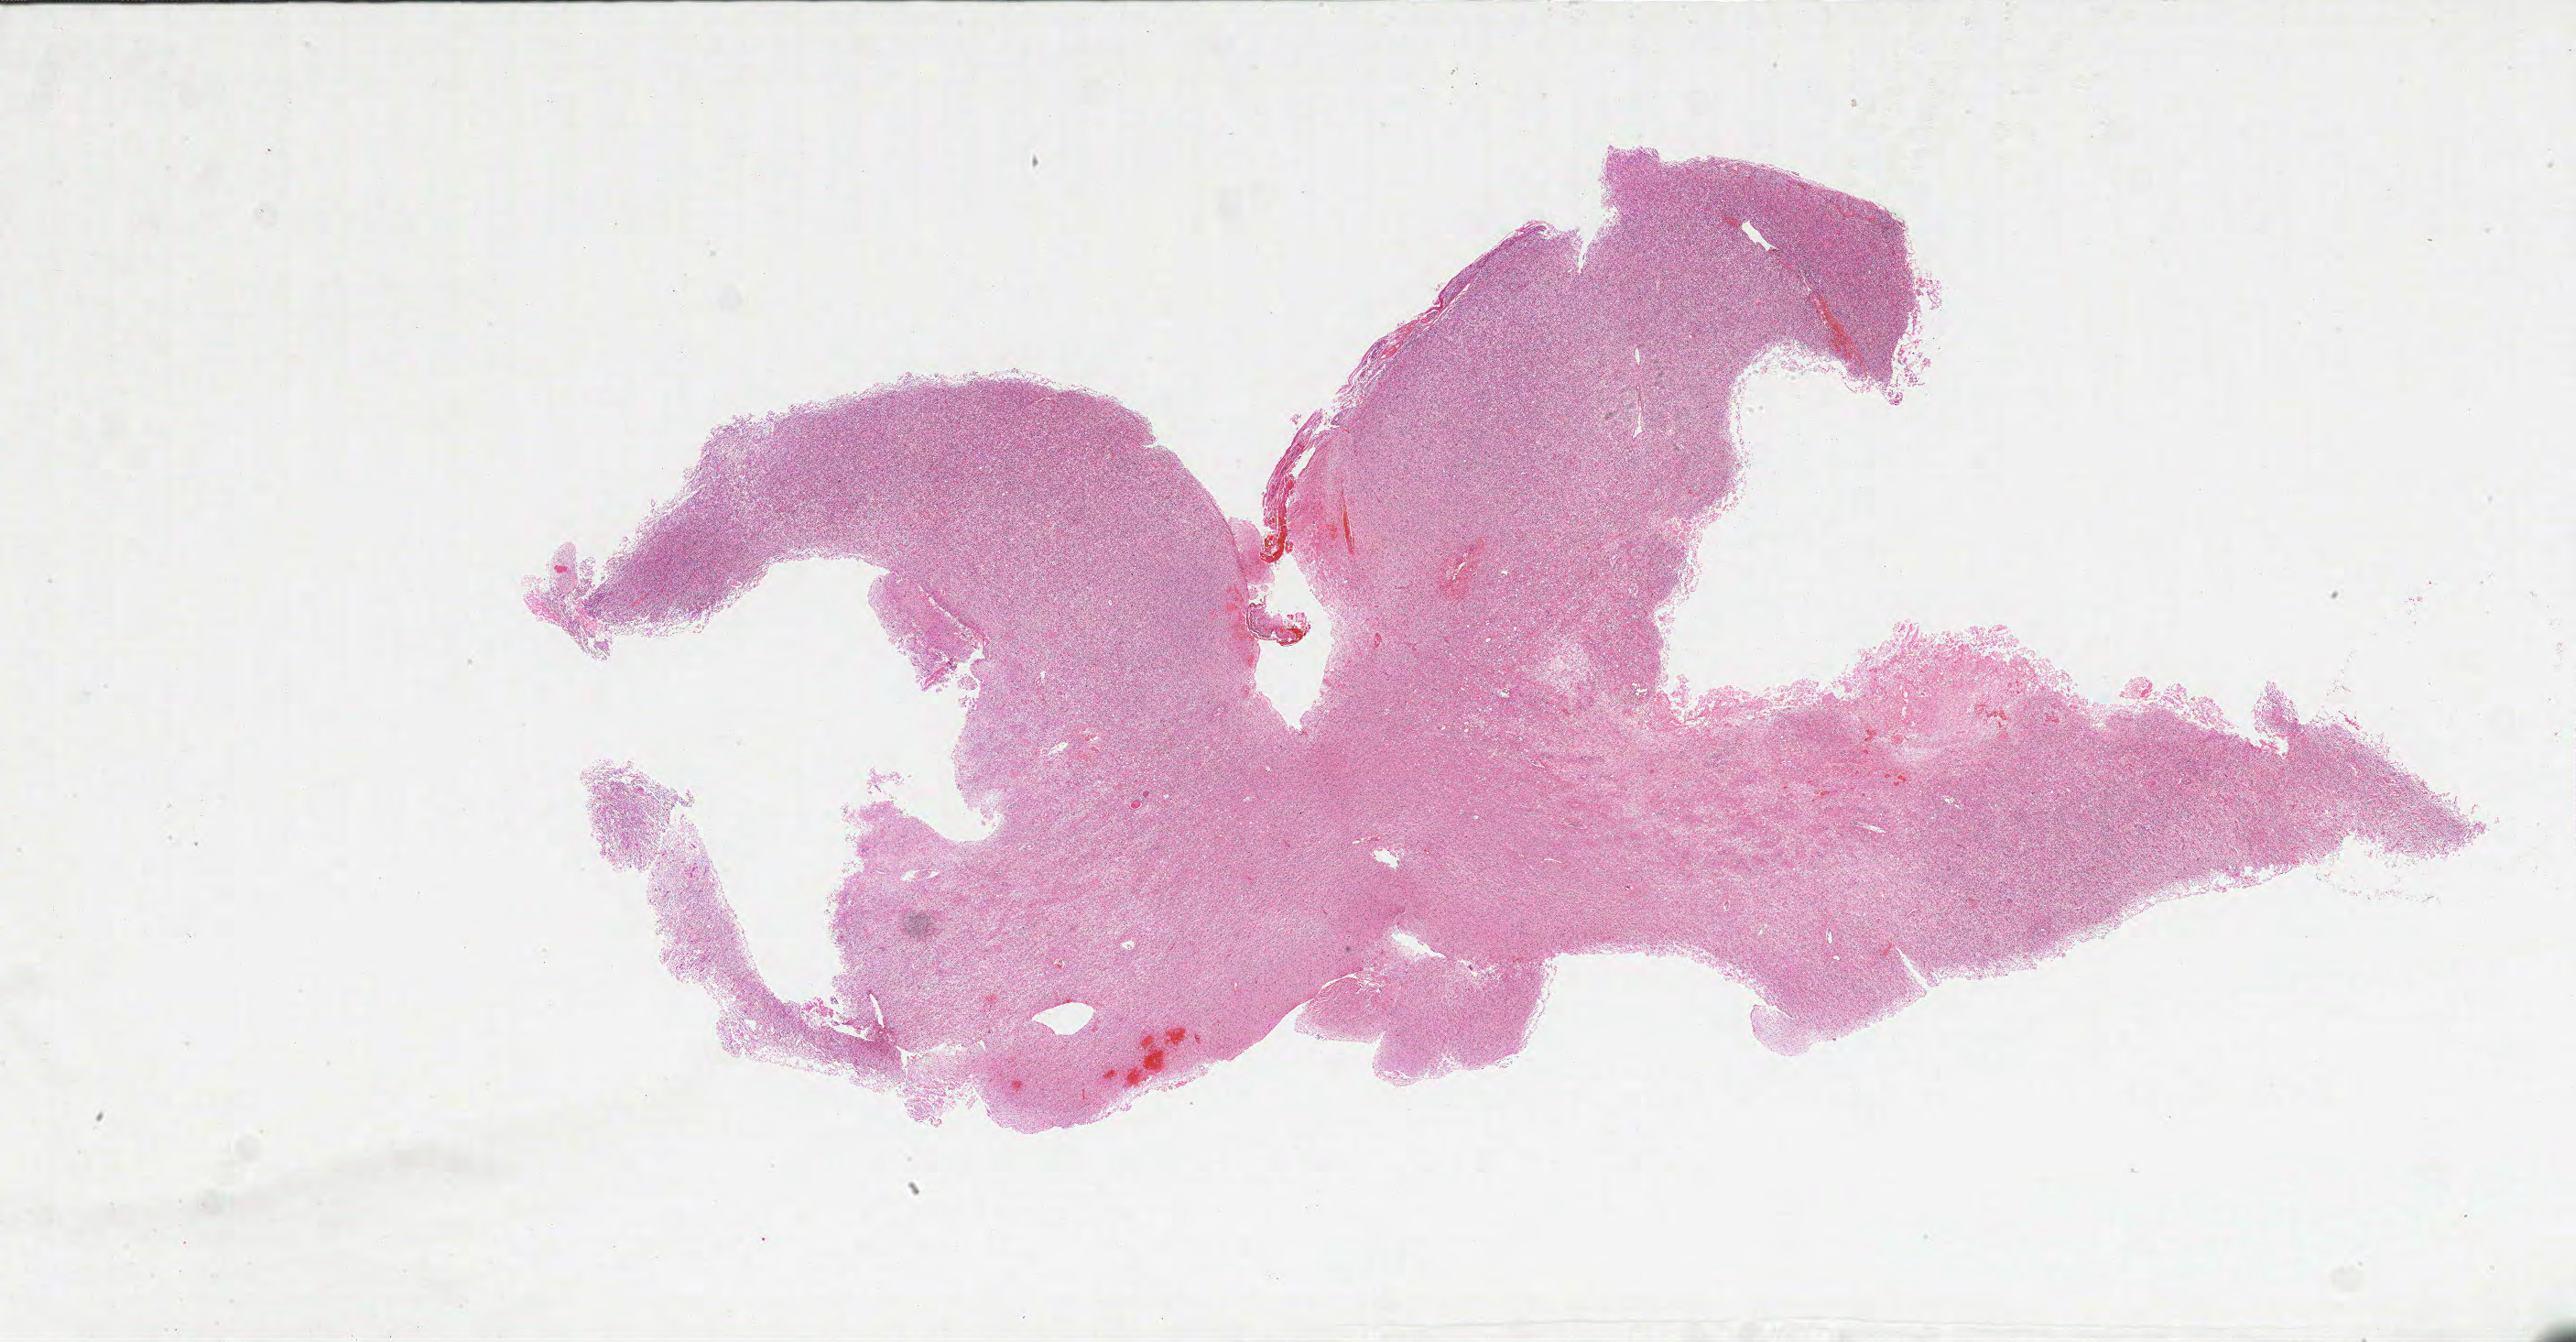
Digitized H&E-stained tissue section (whole slide), whole scanned area (about 45.0 x 23.4 mm, from a 20x scan) shown as a low-resolution overview. Formalin-fixed paraffin-embedded (FFPE) diagnostic section. Brain, primary tumour sample. Female, age 38 years at initial diagnosis.
• pathologic diagnosis: Glioblastoma